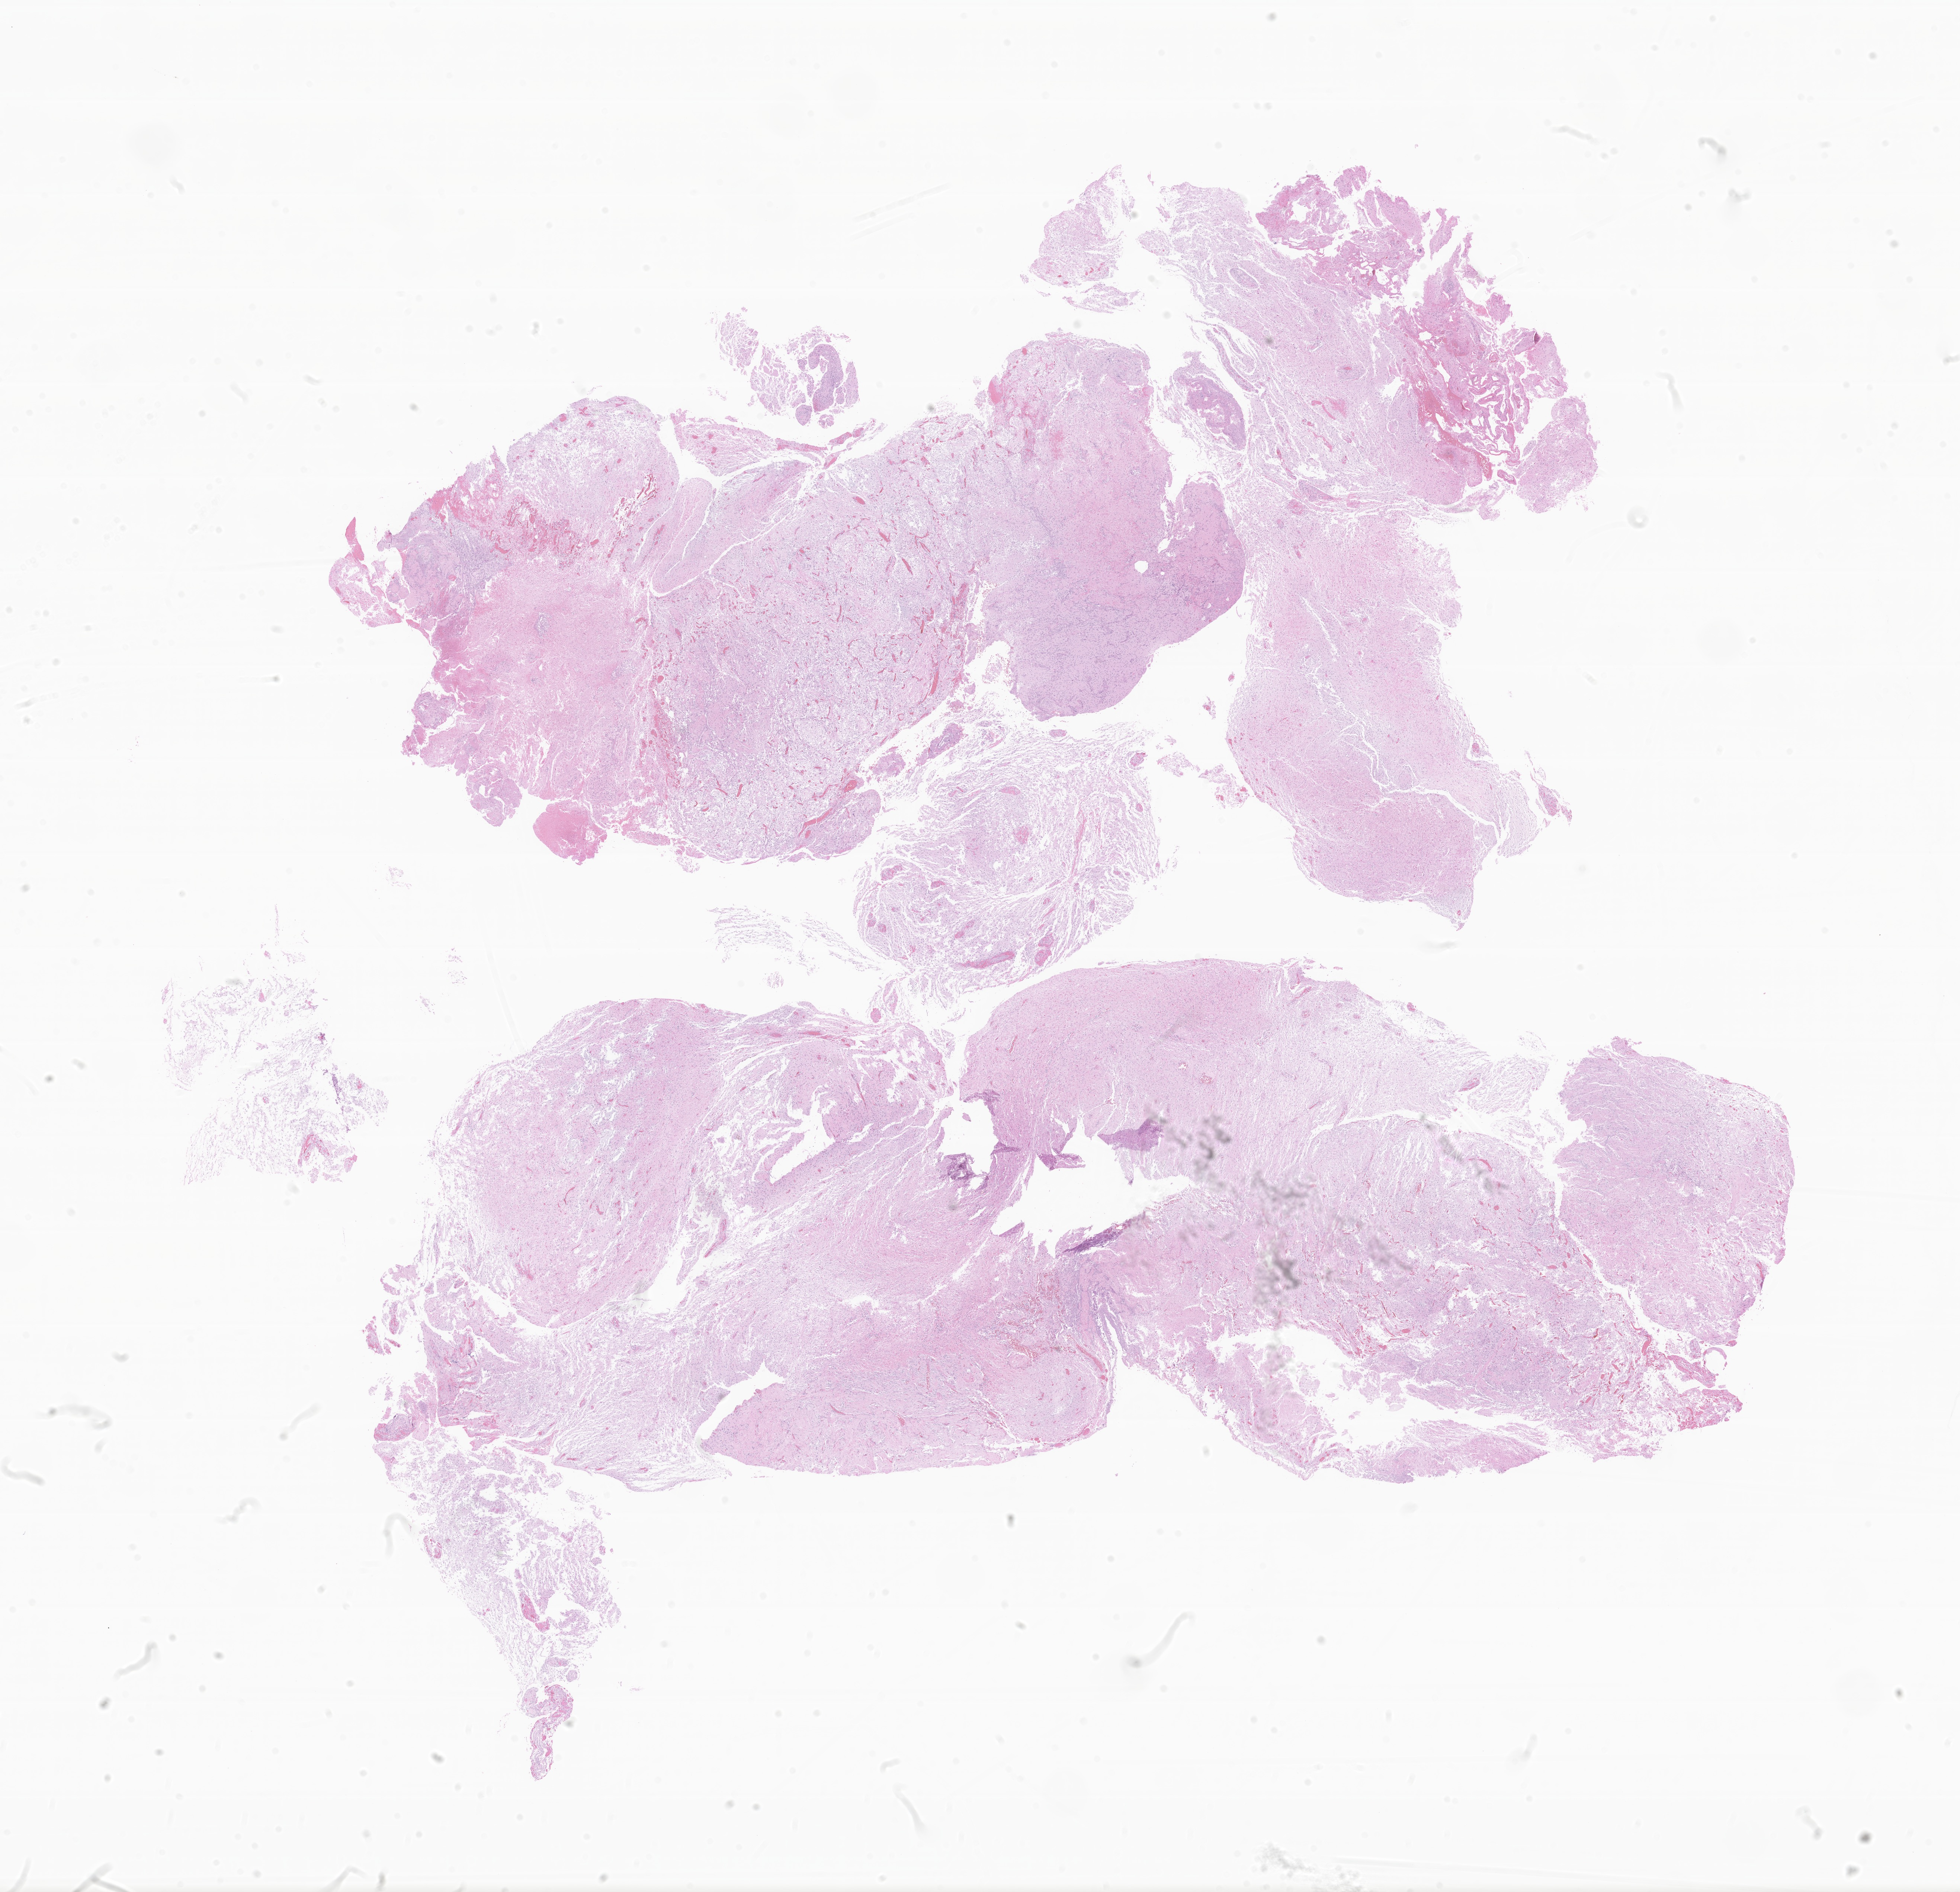
H&E whole-slide image of tumor tissue from the brain, whole scanned area (about 22.2 x 21.4 mm) shown as a low-resolution overview, FFPE section. Patient female; age 58 months (4 years 10 months).
Diagnosis (ICD-O-3 morphology term): Pilocytic astrocytoma.